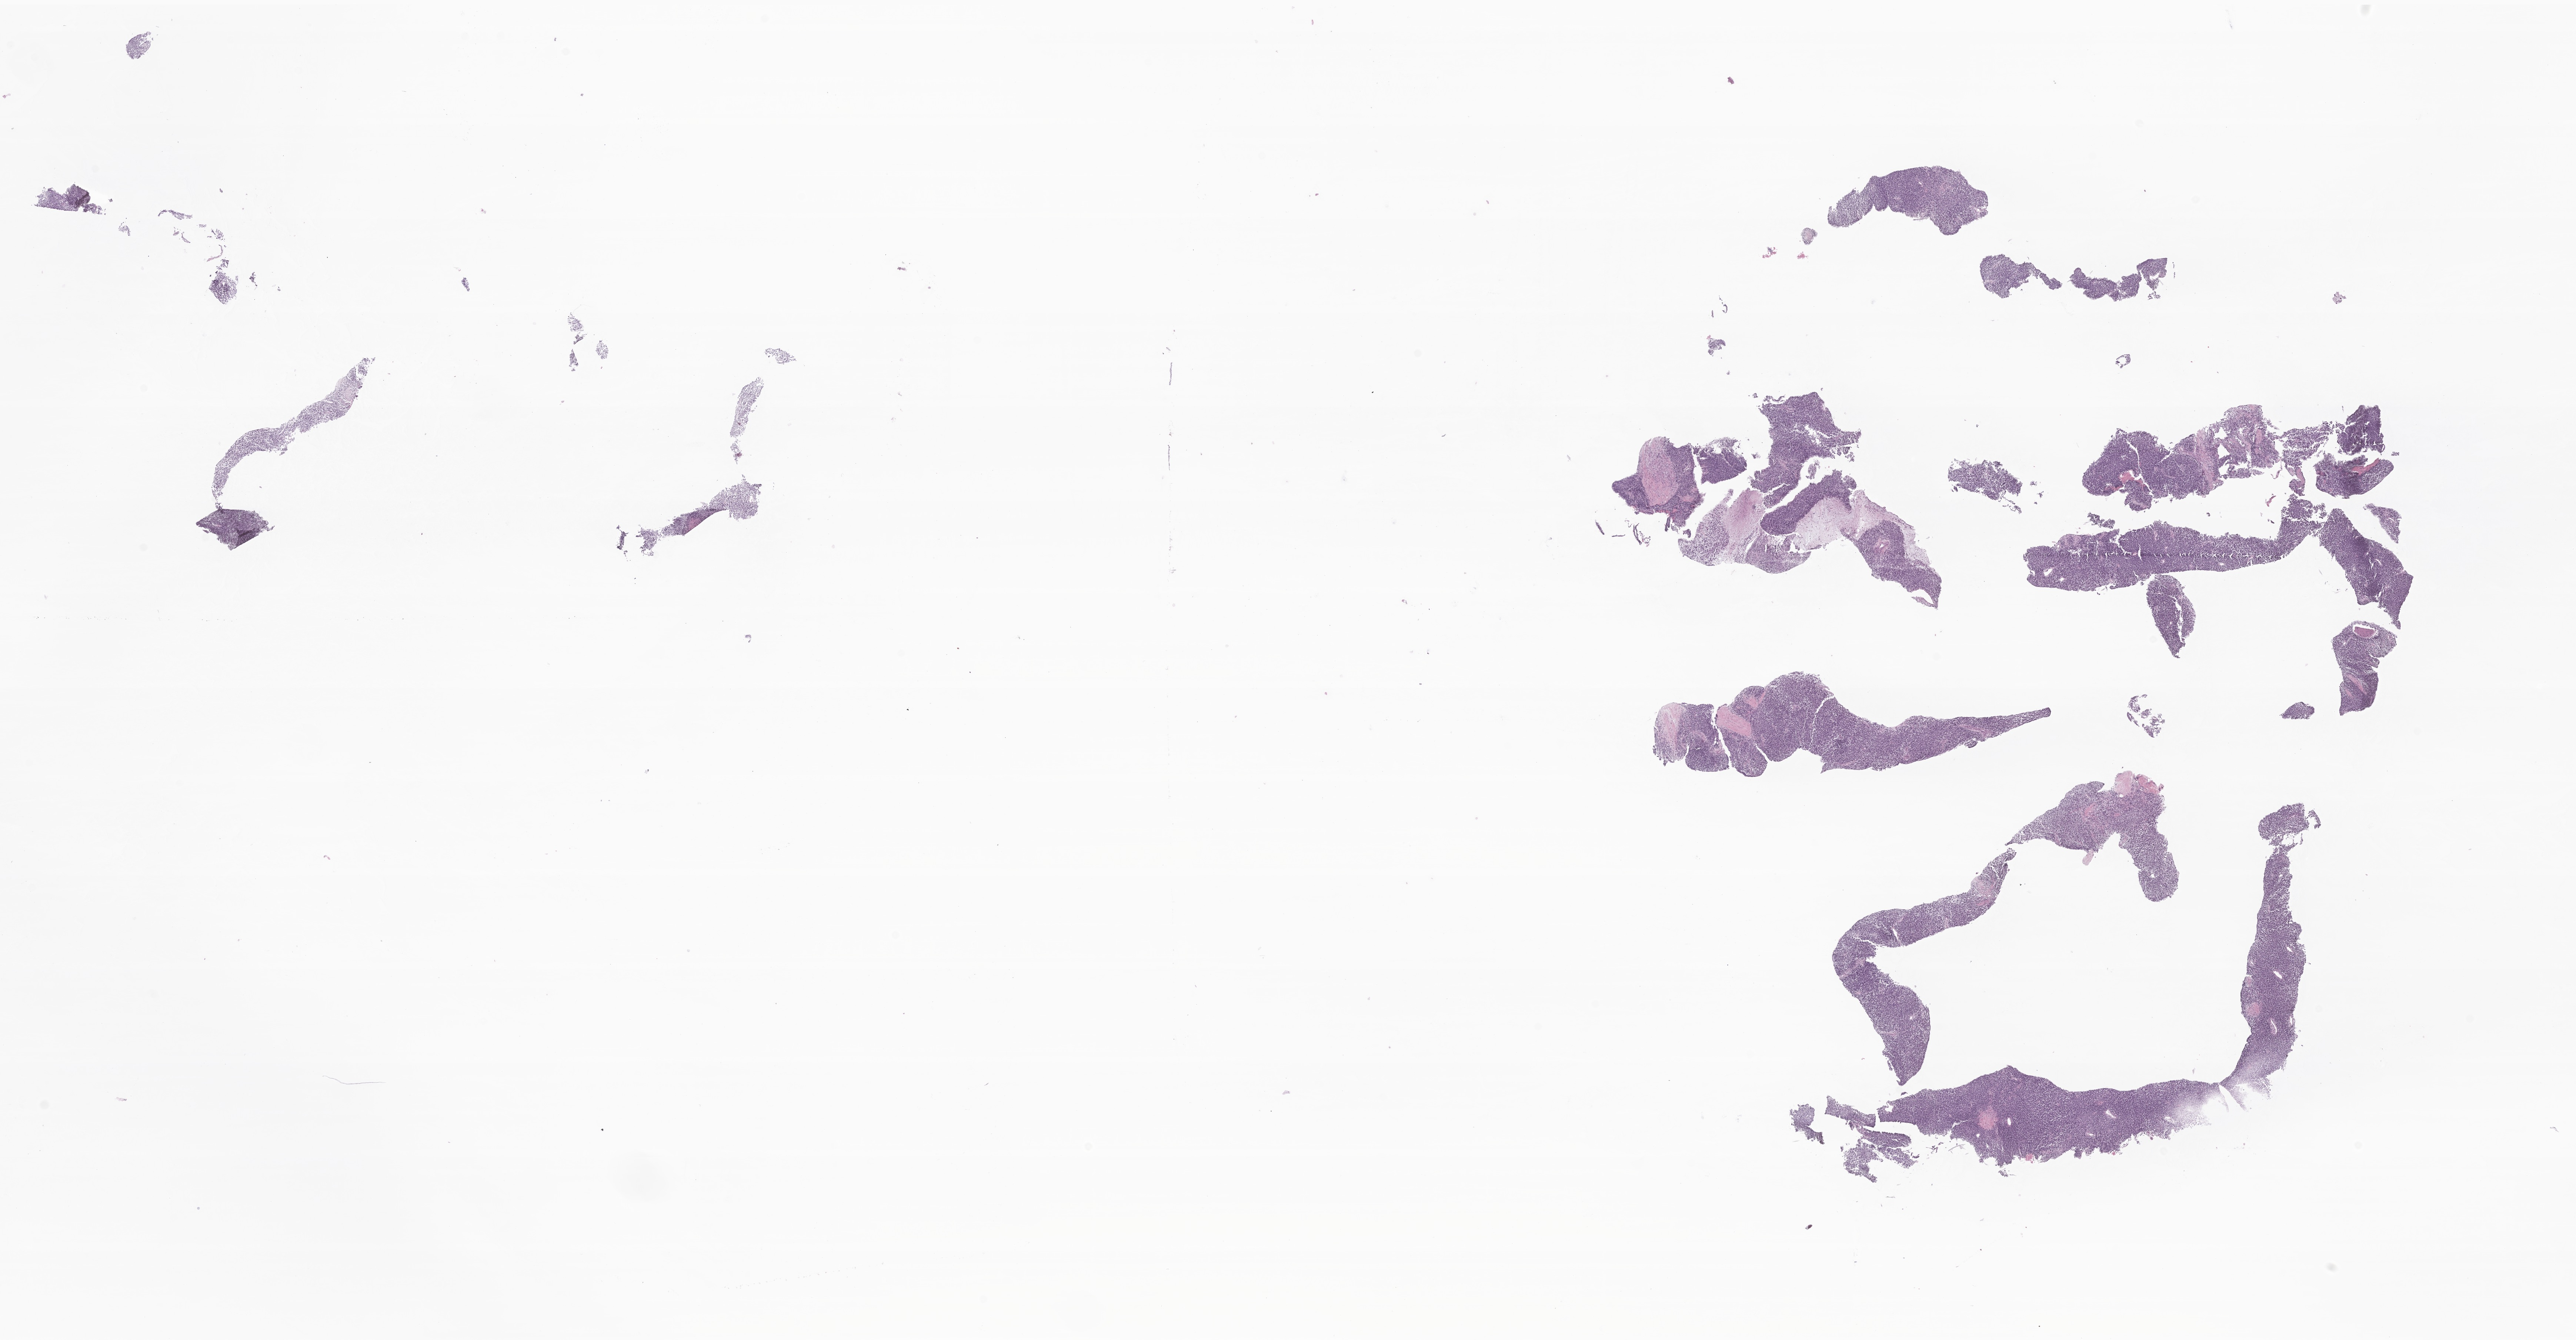
Haematoxylin and eosin whole-slide image of tumor tissue from the soft tissue of trunk, low-resolution overview of the scanned area, about 29.3 x 15.3 mm; formalin-fixed paraffin-embedded section. Female patient, age 76 months (6 years 4 months).
* recorded diagnosis: Embryonal rhabdomyosarcoma, NOS